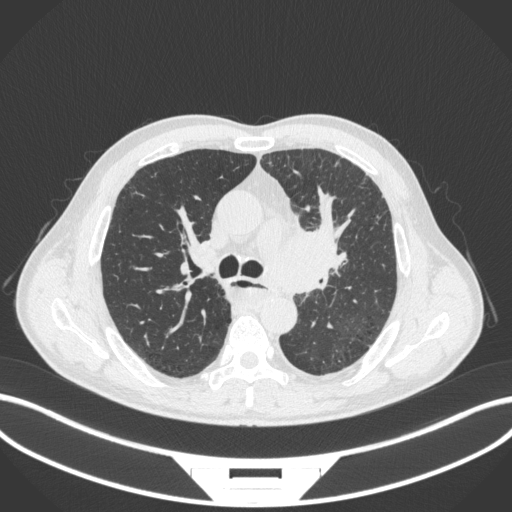
Chest CT, one axial slice; position 247 of 411 along the scan axis; lung window (W 1500 / L -600 HU); 1 mm slice thickness; 512 × 512 image matrix, field of view 400 × 400 mm. Male patient, age 57 years. Case-level facts recorded for this patient, not image findings: clinical TNM (as recorded): T2a N1 M0.
Annotated regions visible in this slice (bounding box drawn by a radiologist):
- lung tumour (recorded histology: squamous cell carcinoma): bounding box (x1, y1, x2, y2) in pixels: (264, 217, 348, 297)